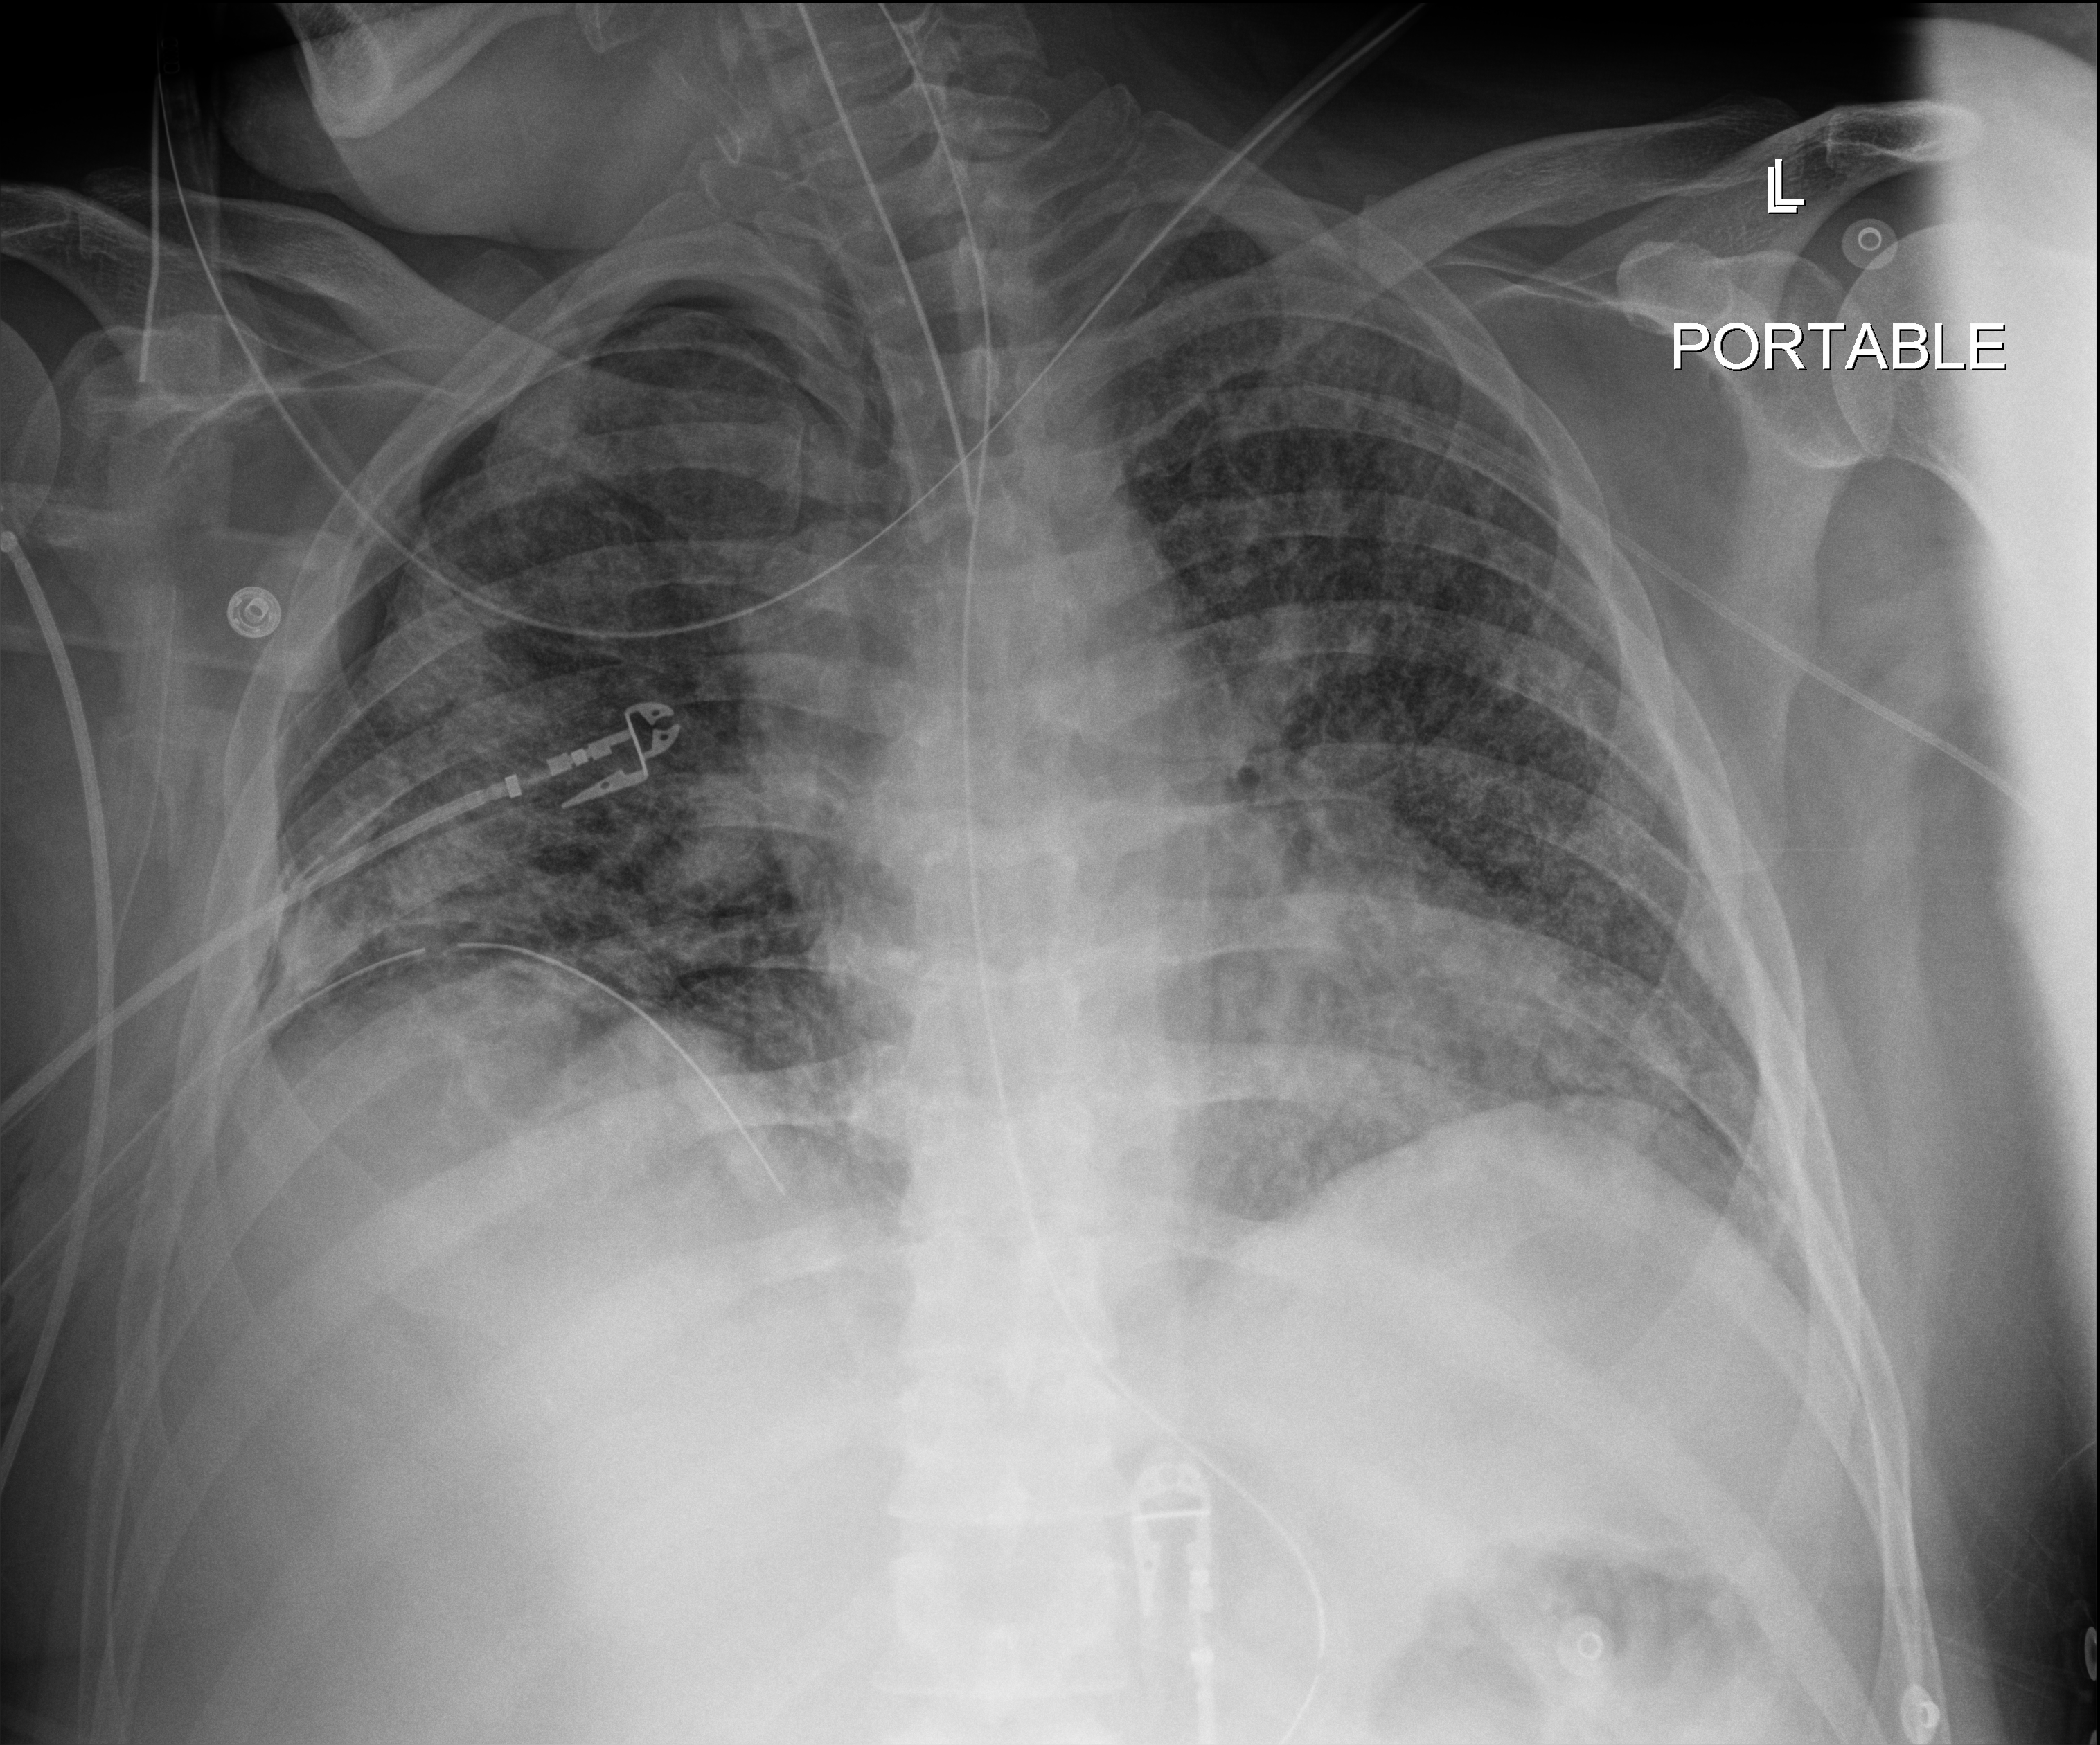
Chest X-ray (portable); anteroposterior (AP) projection. Patient hospitalised with COVID-19; male, aged 18–59 years.
Hospital-stay facts (about this admission, not read from this image; timing relative to this image not recorded): length of hospital stay: 80 days; chronic kidney disease (admission record): no; admitted to intensive care during this hospital stay: yes.